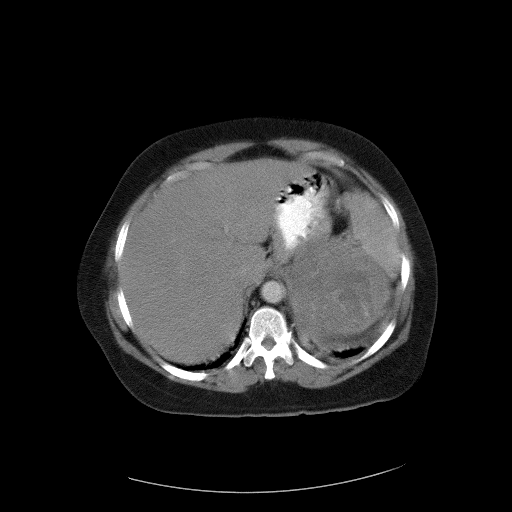
Contrast-enhanced abdominal CT, one axial slice; slice 80 of 90 in the series (ordered by position); reconstruction kernel FC01; intravenous contrast given; soft-tissue window (W 400 / L 40 HU); 512 × 512 image matrix, field of view 480 × 480 mm. Female patient, age 55 years. From the clinical record (not read from this slice): diagnosis: adrenocortical carcinoma; tumour side: left adrenal; tumour size at pathology: 22 cm; Ki-67 index: 10 %; stage (as recorded): 3.
Structures marked on this image (semi-automatically segmented with operator editing):
- mass: bounding box (x1, y1, x2, y2) in pixels: (291, 240, 388, 339)